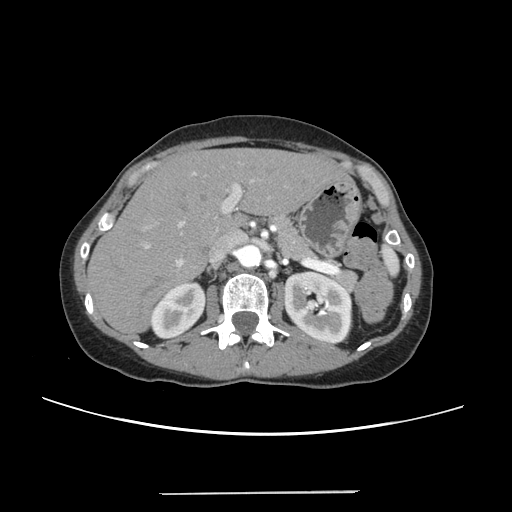
Contrast-enhanced abdominal CT, one axial slice. Intravenous contrast given. Soft-tissue window (W 400 / L 40 HU). 1.25 mm slice thickness. 512 × 512 image matrix, field of view 371 × 371 mm. Female patient, age 60 years. From the clinical record (not read from this slice): diagnosis: colorectal cancer liver metastases, imaged before liver resection; multiple liver metastases: no; largest metastasis: 1.5 cm; disease in both lobes: no.
Outlined on this slice (outlined manually by an expert reader):
- liver: bounding box [x1, y1, x2, y2] px = [90, 150, 345, 331]
- planned liver remnant (the part of the liver to remain after resection): [90, 150, 344, 331]
- portal vein (with intrahepatic branches): [144, 171, 257, 266]